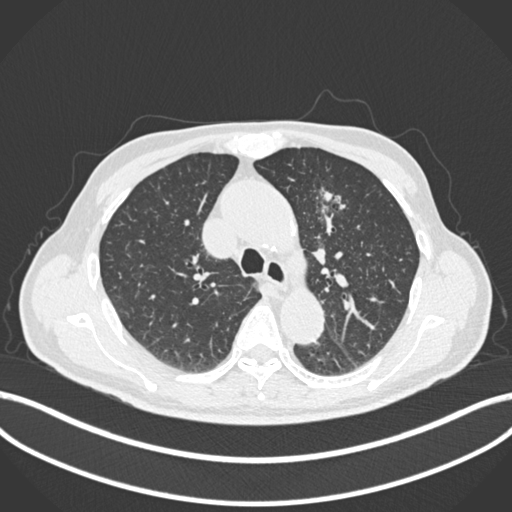
Chest CT, one axial slice. Position 173 of 261 along the scan axis. 120 kVp. Lung window (W 1500 / L -600 HU). 1 mm slice thickness. 512 × 512 image matrix. Patient: male, 74 years. Case-level facts recorded for this patient, not image findings: clinical TNM (as recorded): T2b N0 M1c.
Structures marked on this image (rectangle marked by the reading radiologist):
- lung tumour (recorded histology: adenocarcinoma): box from (x=316, y=182) to (x=347, y=221) px